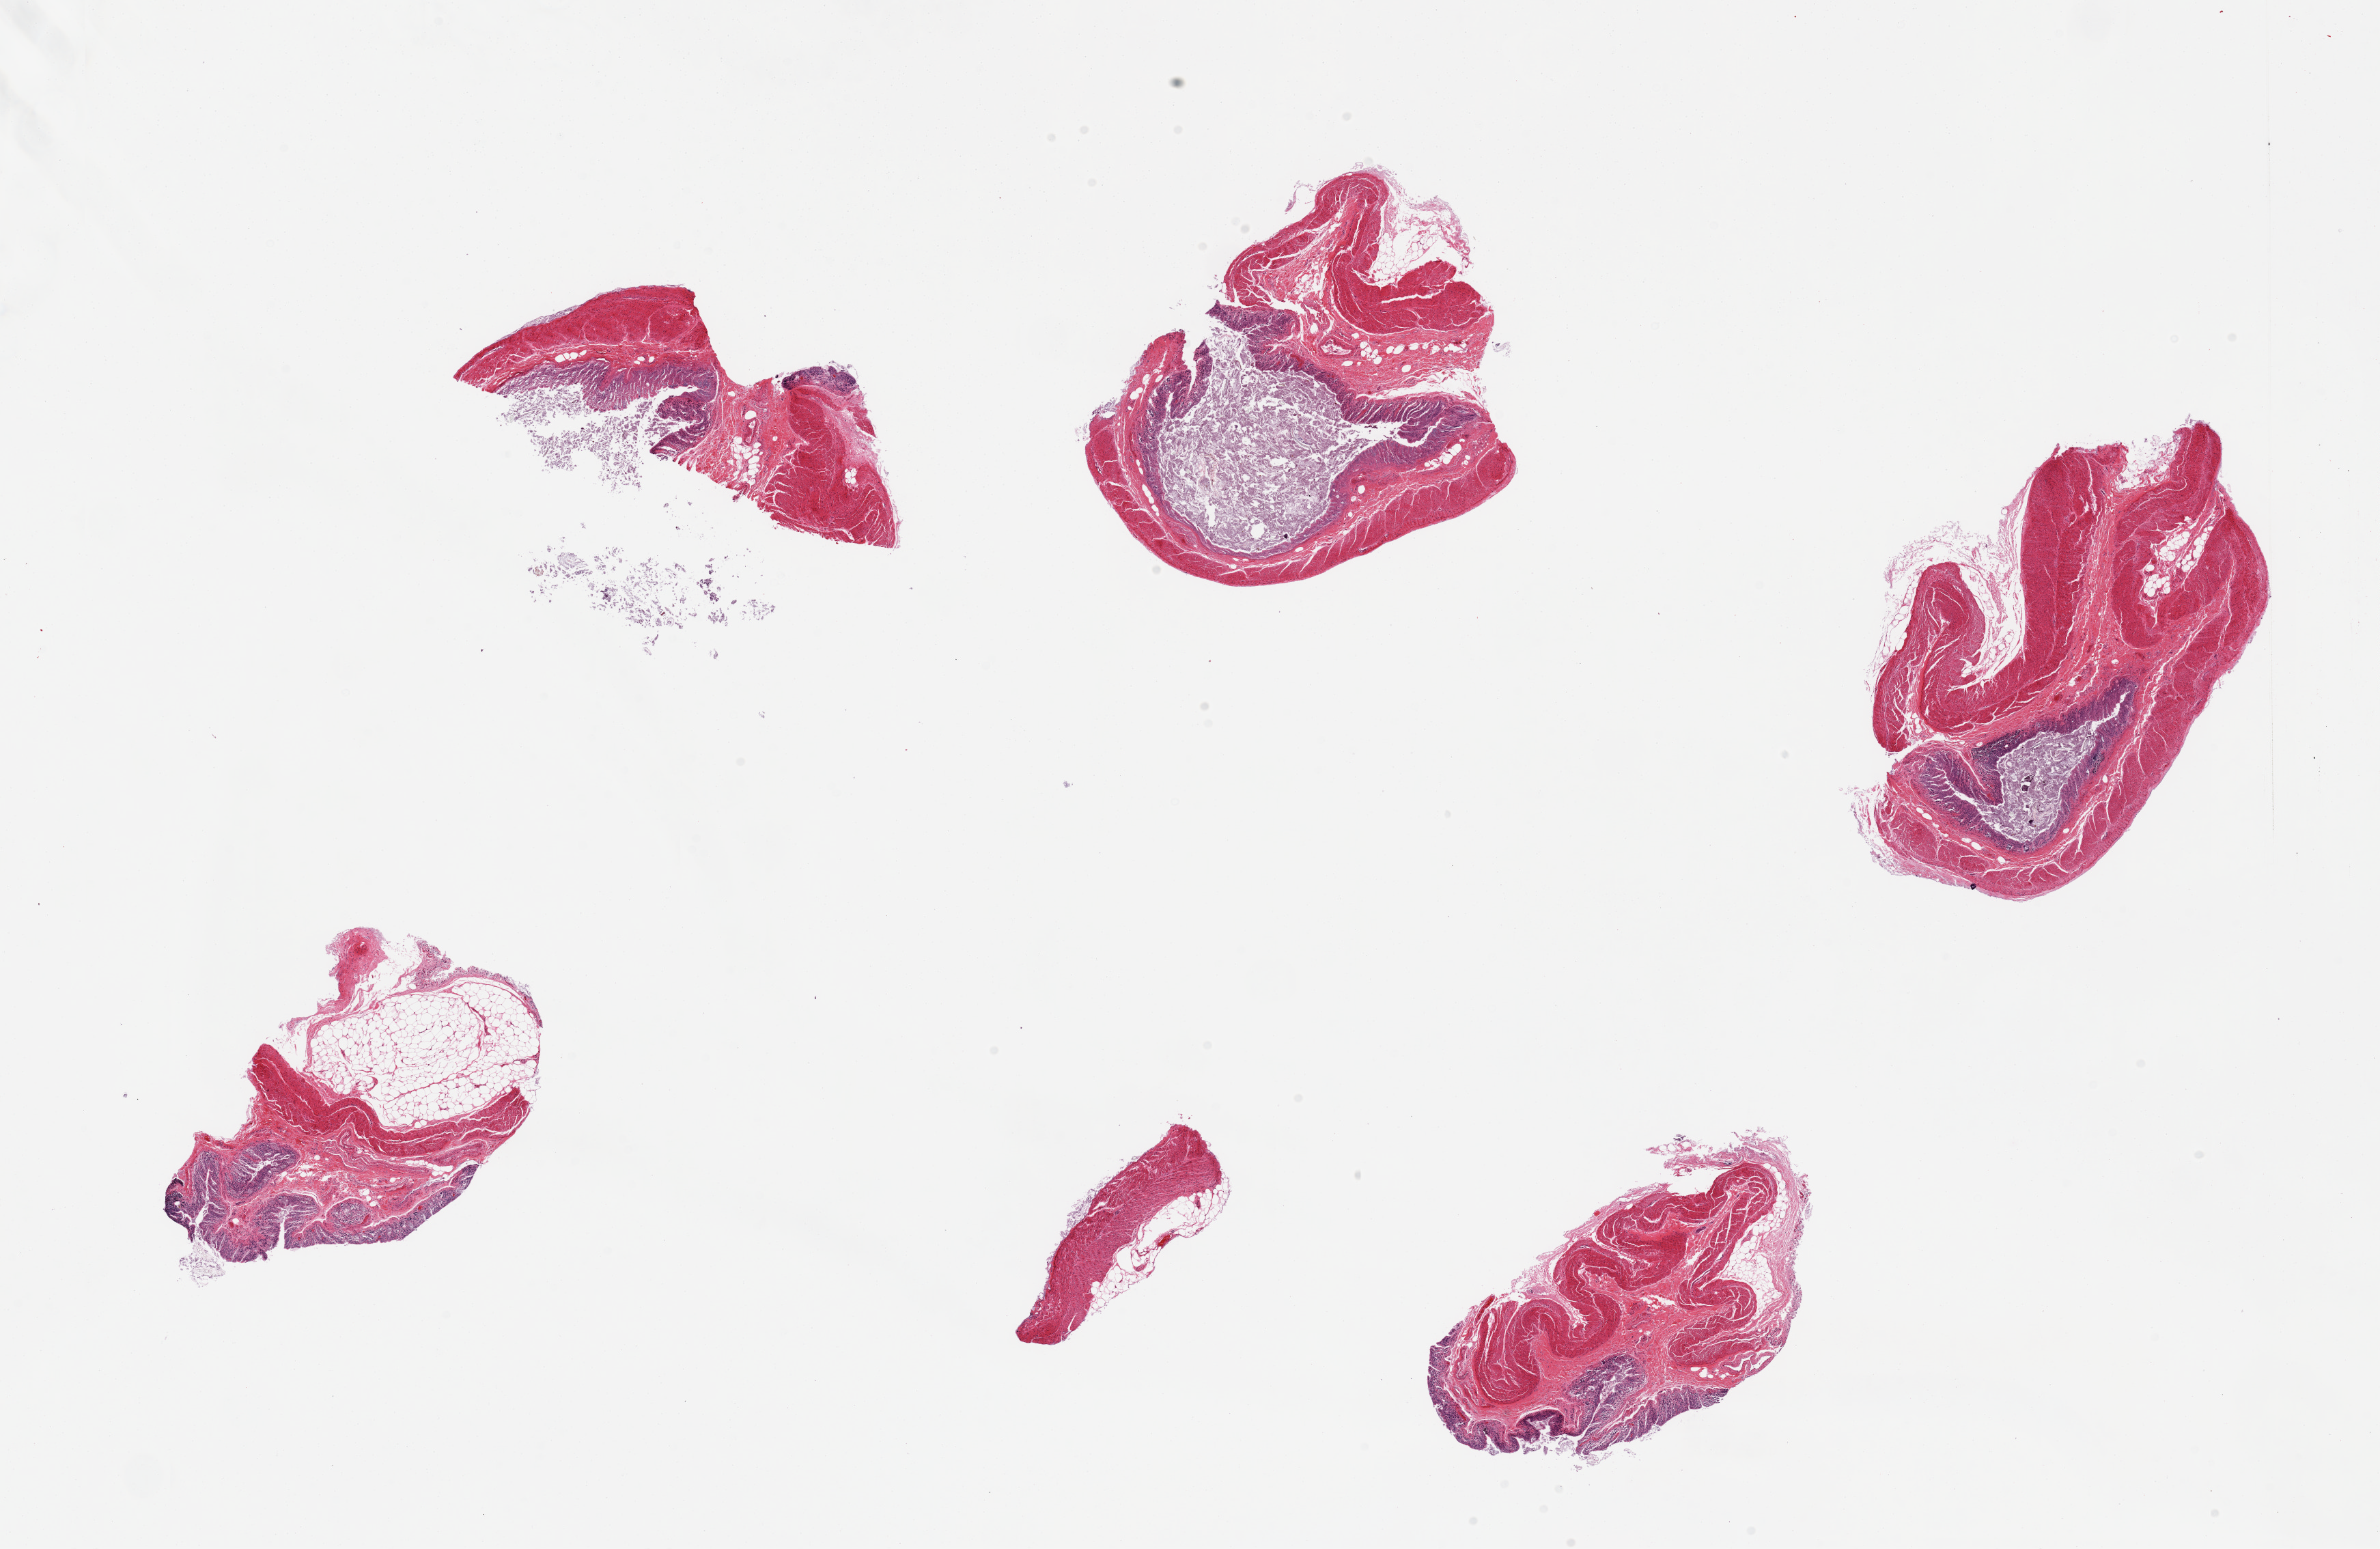
Digitized haematoxylin and eosin-stained section — low-resolution overview of the scanned area, about 27.6 x 17.9 mm (acquisition: 20x scan), PAXgene-fixed paraffin-embedded (PFPE) section, sampled site (target tissue): transverse colon, donor tissue sample.
Review note (as recorded): 6 pieces, muscularis and severely autolyzed mucosa.